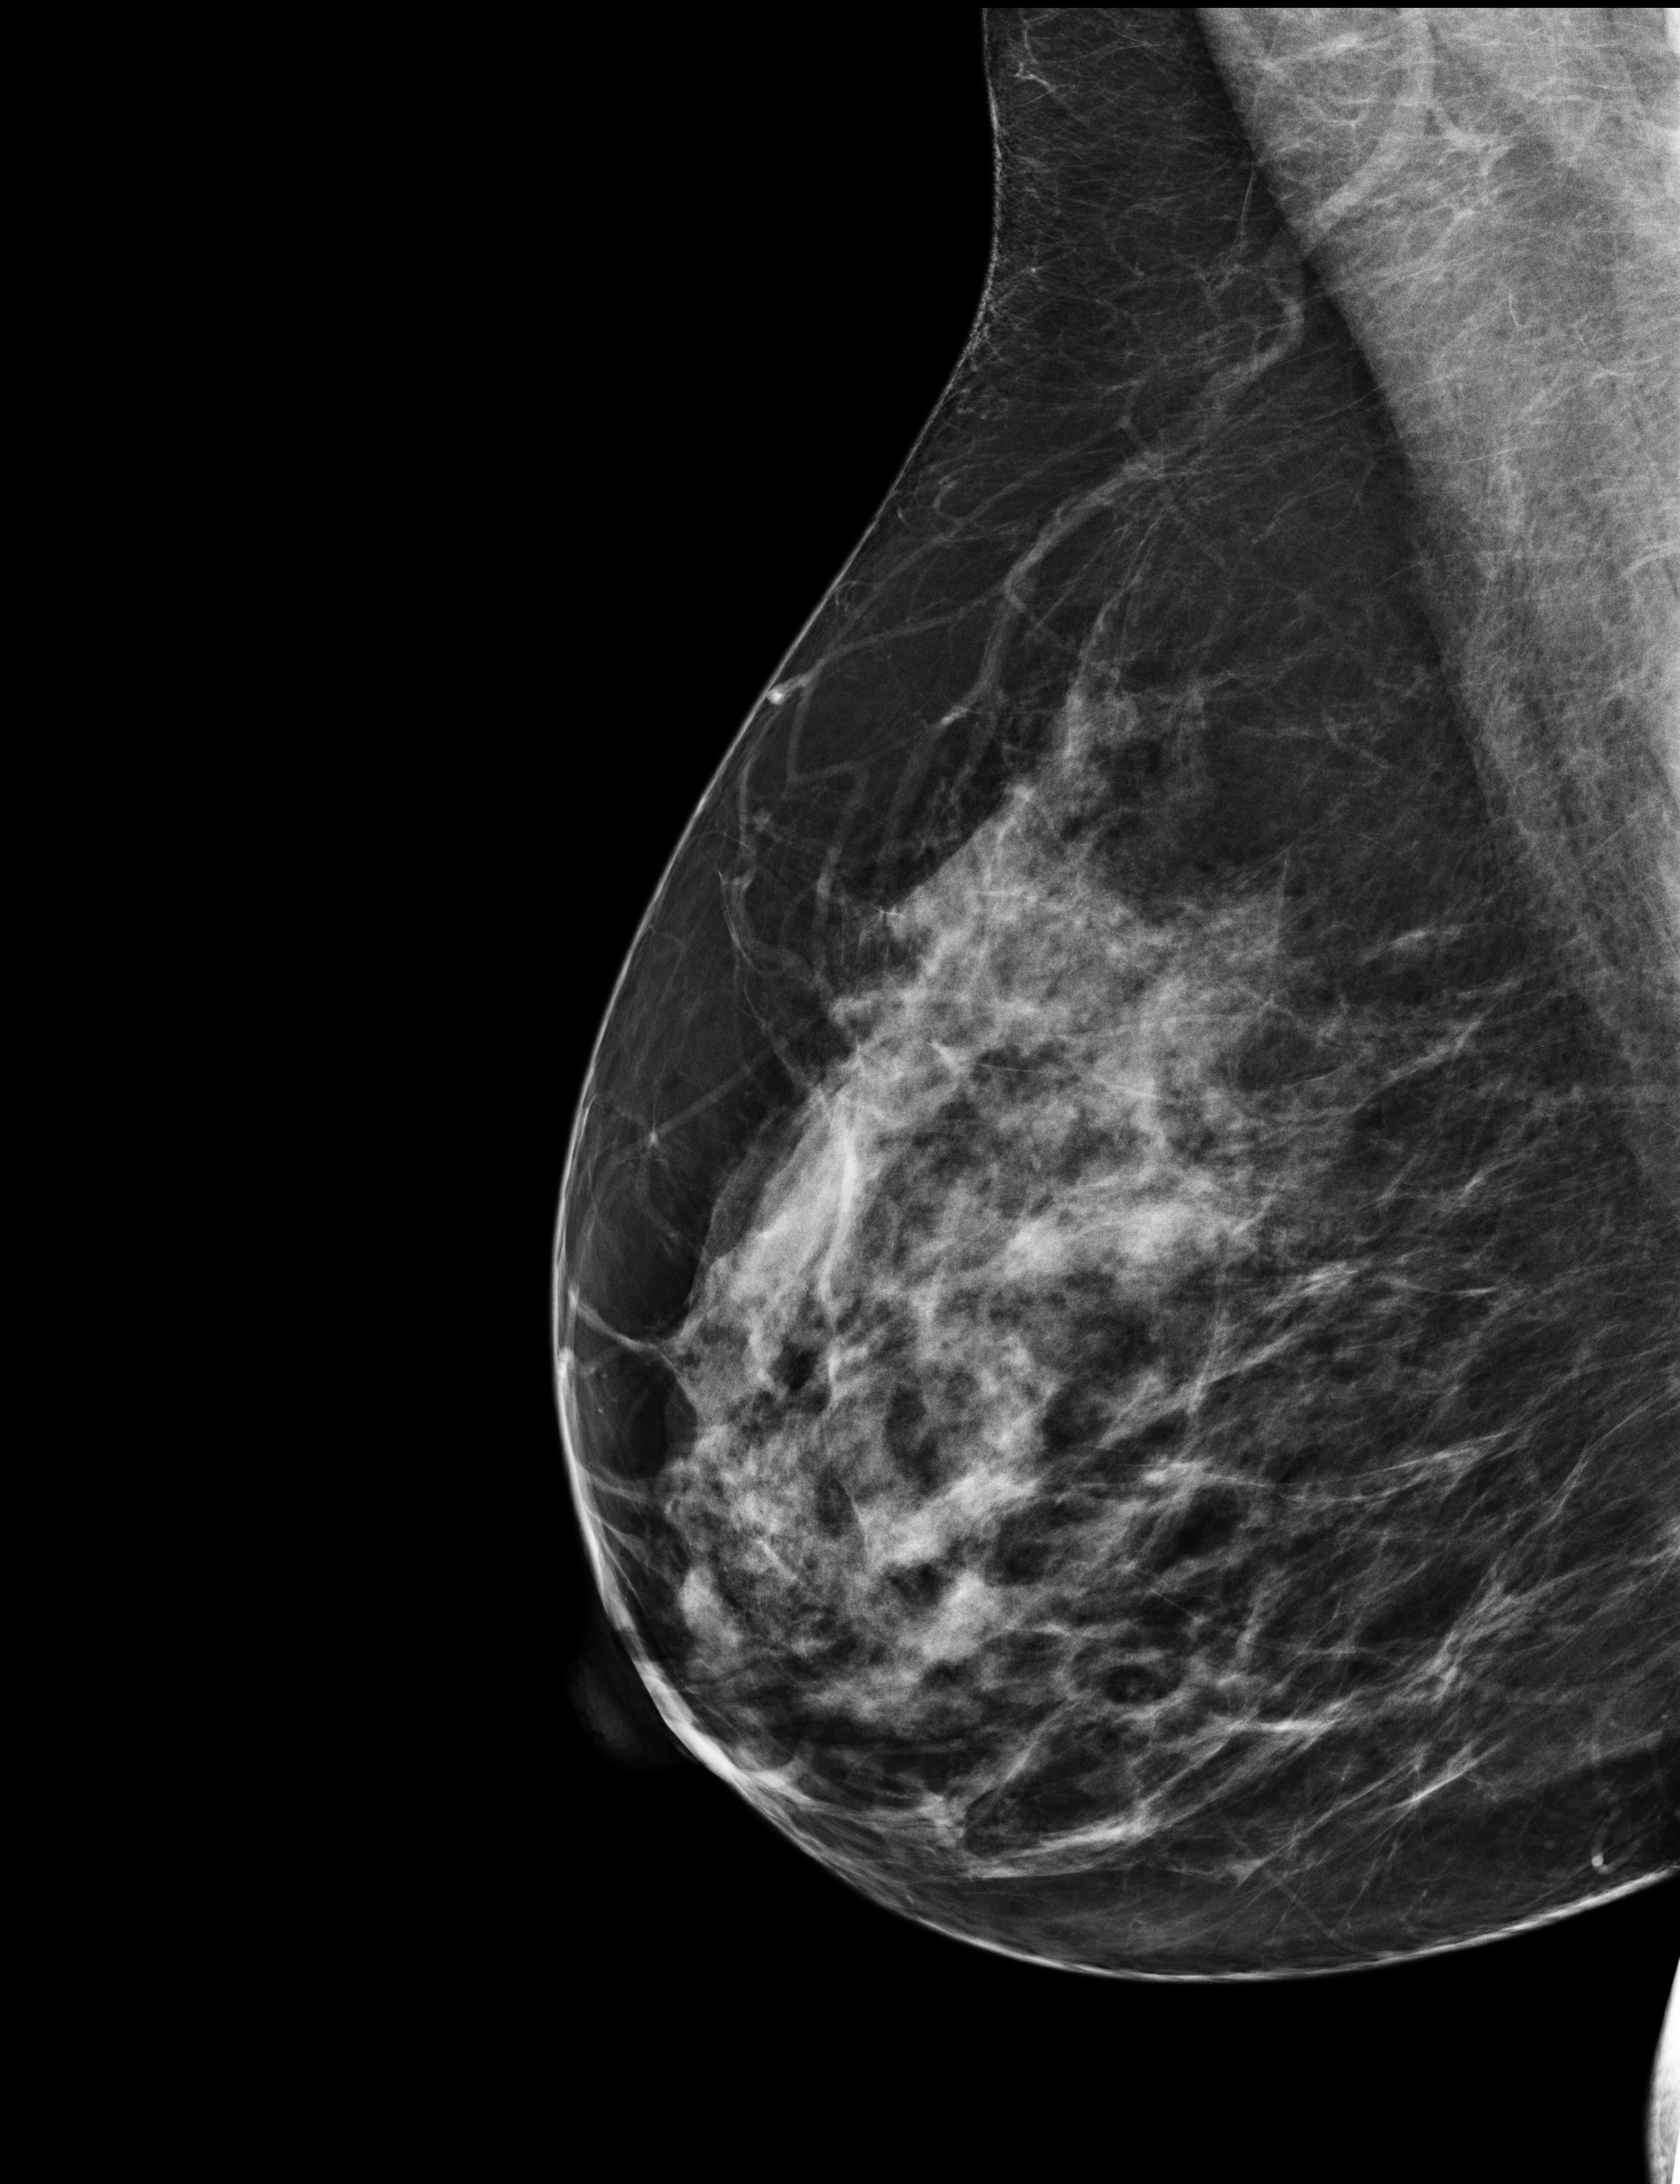
Screening examination, compressed breast thickness 67 mm, system: Selenia Dimensions. Patient aged 42 years (female).
Image type: full-field digital mammogram. Breast: right. Projection: medio-lateral oblique projection.